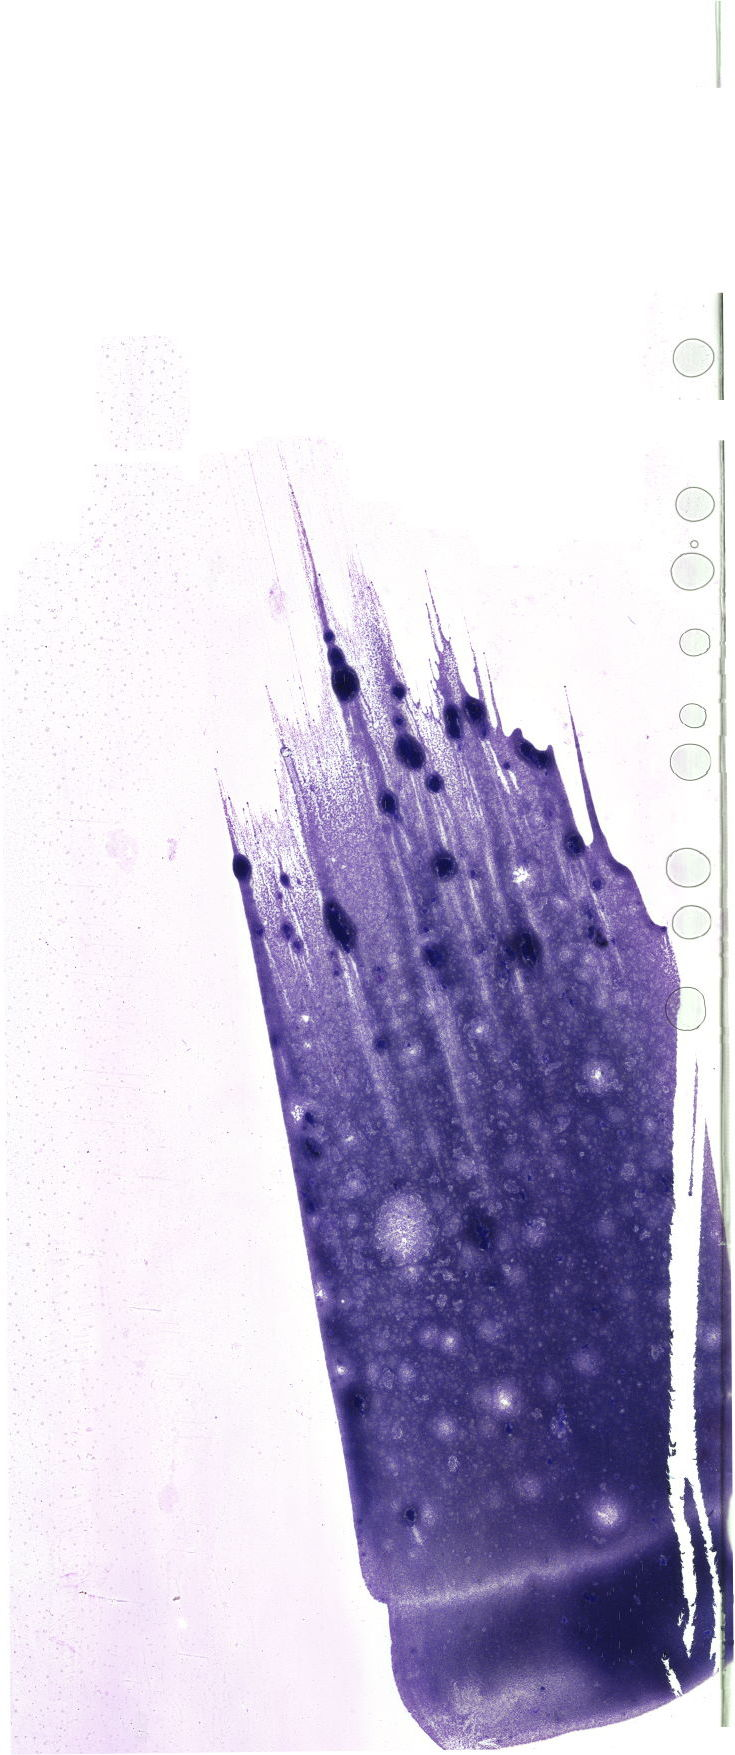
Whole-slide image of a May-Grünwald–Giemsa-stained bone marrow aspirate smear, shown as a low-resolution overview of the whole scanned area (about 20.8 x 49.7 mm). Male patient.
Diagnosis: Chronic Phase Chronic Myeloid Leukemia, BCR-ABL1 Positive.